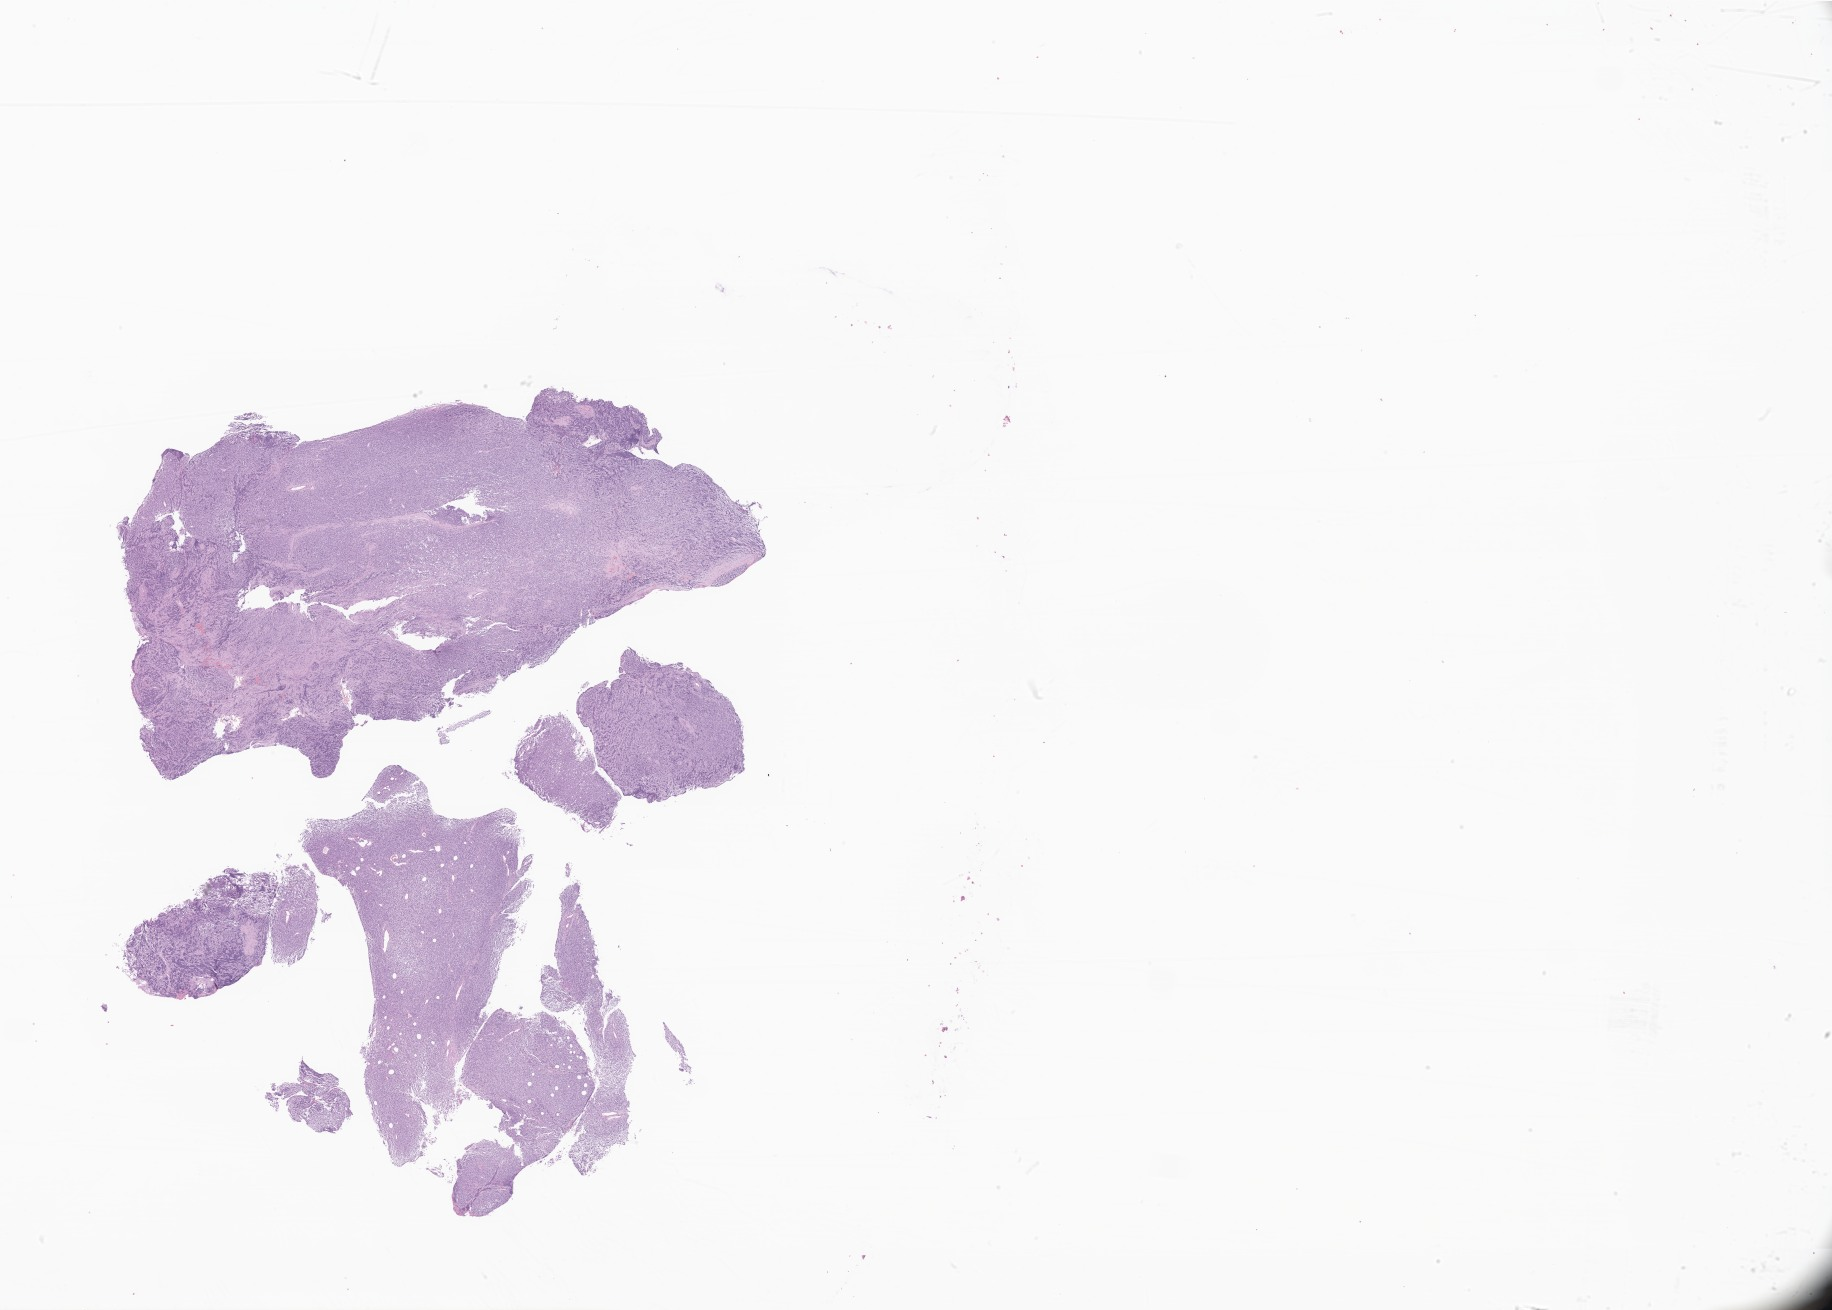
Digitized hematoxylin and eosin (H&E)-stained section of tumor tissue from the soft tissue — whole scanned area (about 30.9 x 22.1 mm) shown as a low-resolution overview. FFPE section. Patient male; age 83 months (6 years 11 months).
Diagnosis: Embryonal rhabdomyosarcoma, NOS.